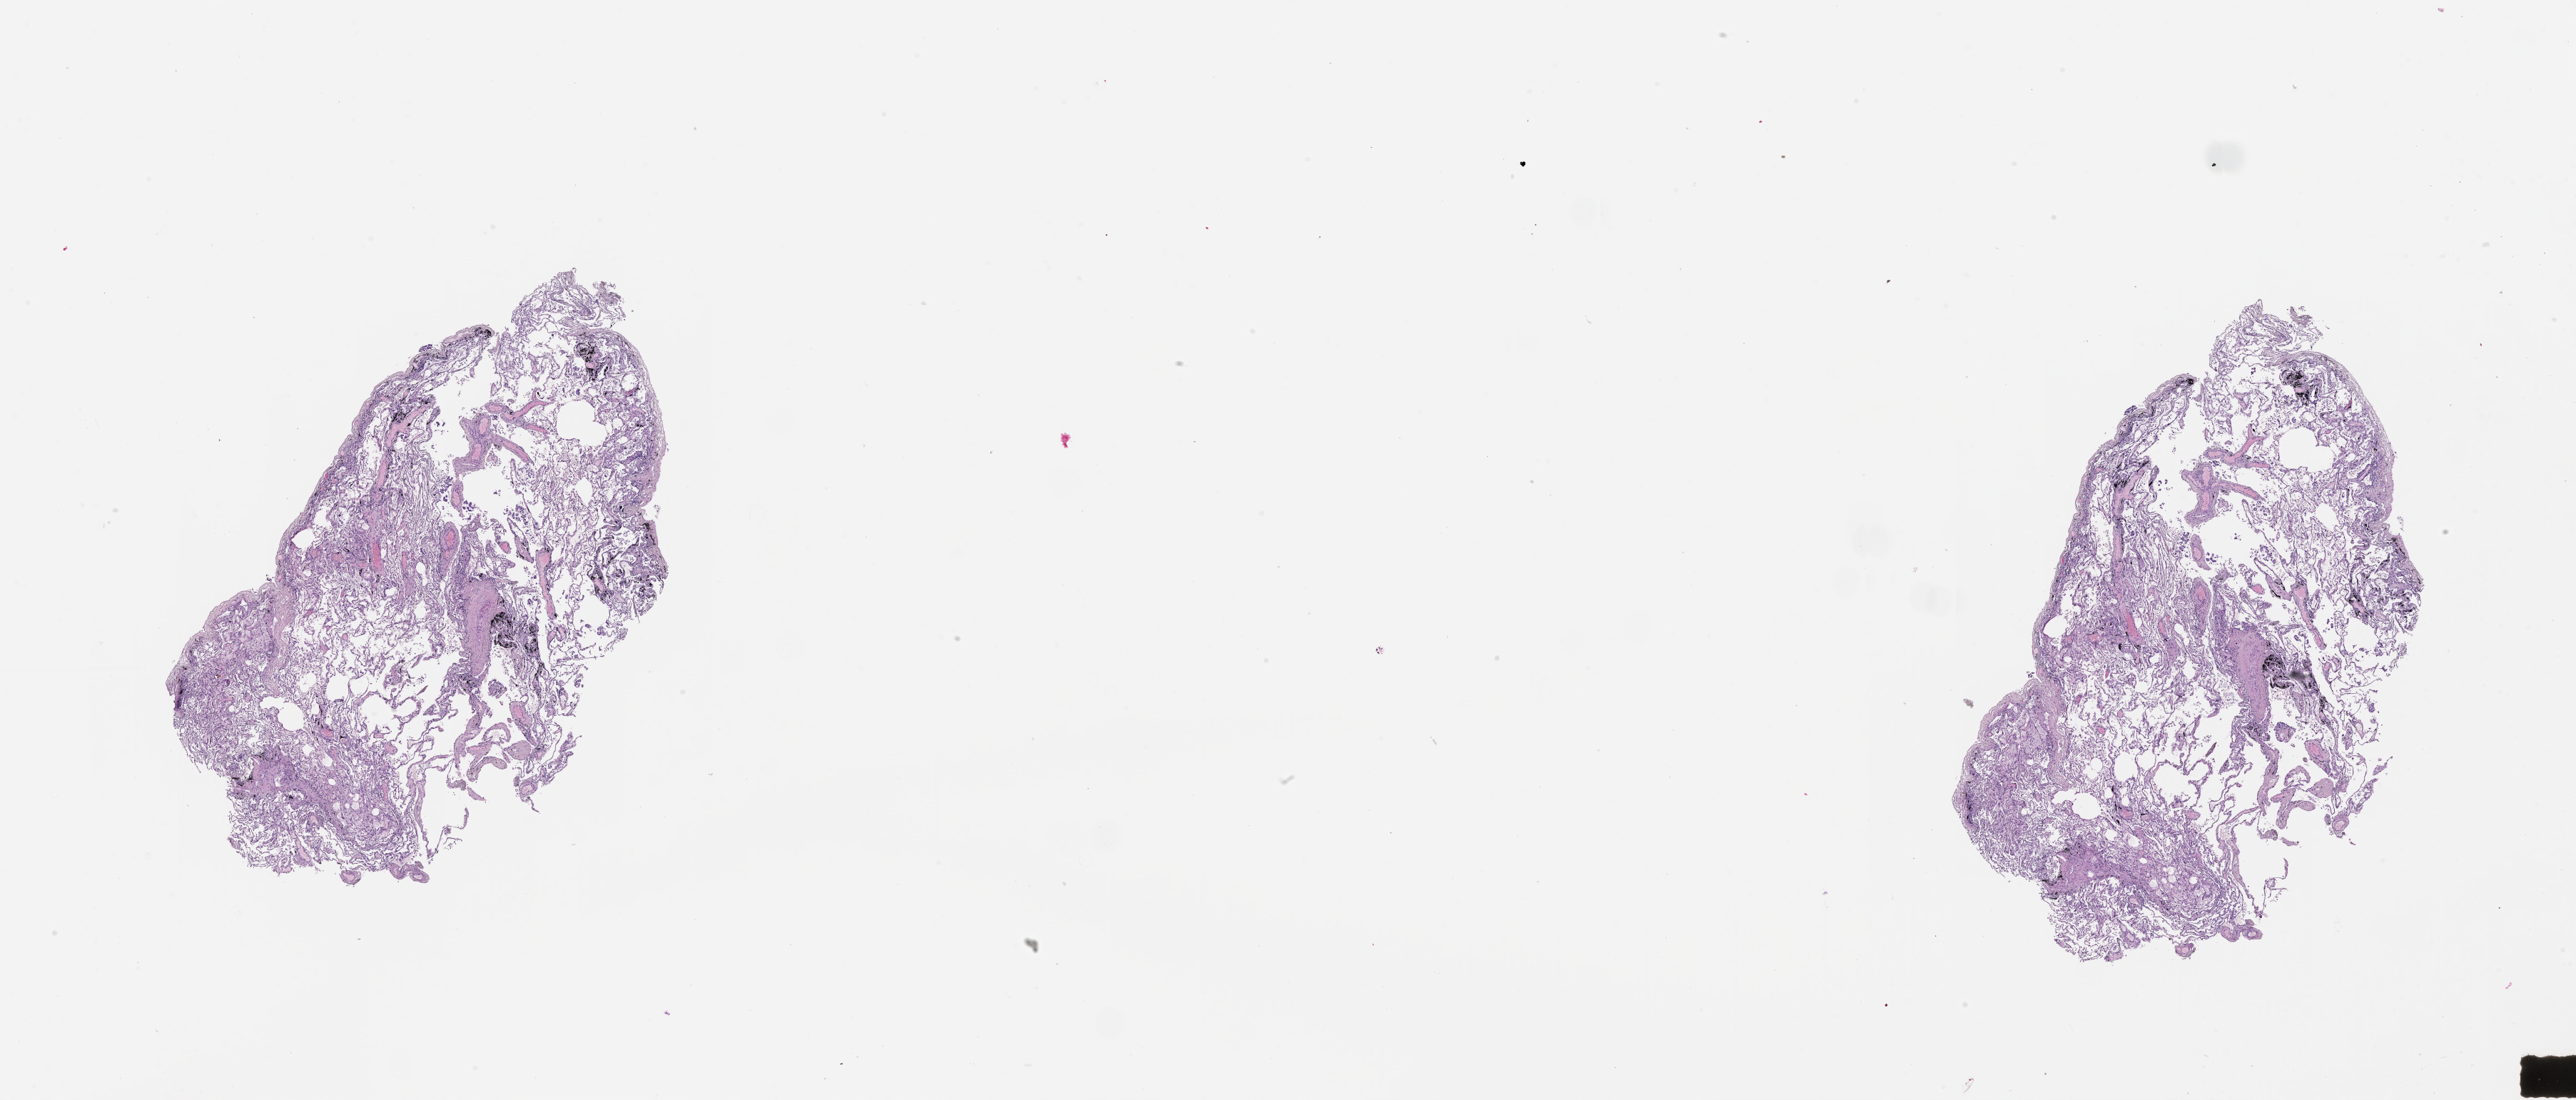
Whole-slide histology image, Hematoxylin and eosin (H&E) stained — a low-resolution overview of the entire scanned area, about 29.1 x 12.4 mm (acquisition: 20x scan). Lung, normal (non-tumour) tissue. Patient: male, age 67 years.
This section: normal (non-tumour) tissue from the same patient. Patient diagnosis: Adenocarcinoma, NOS.